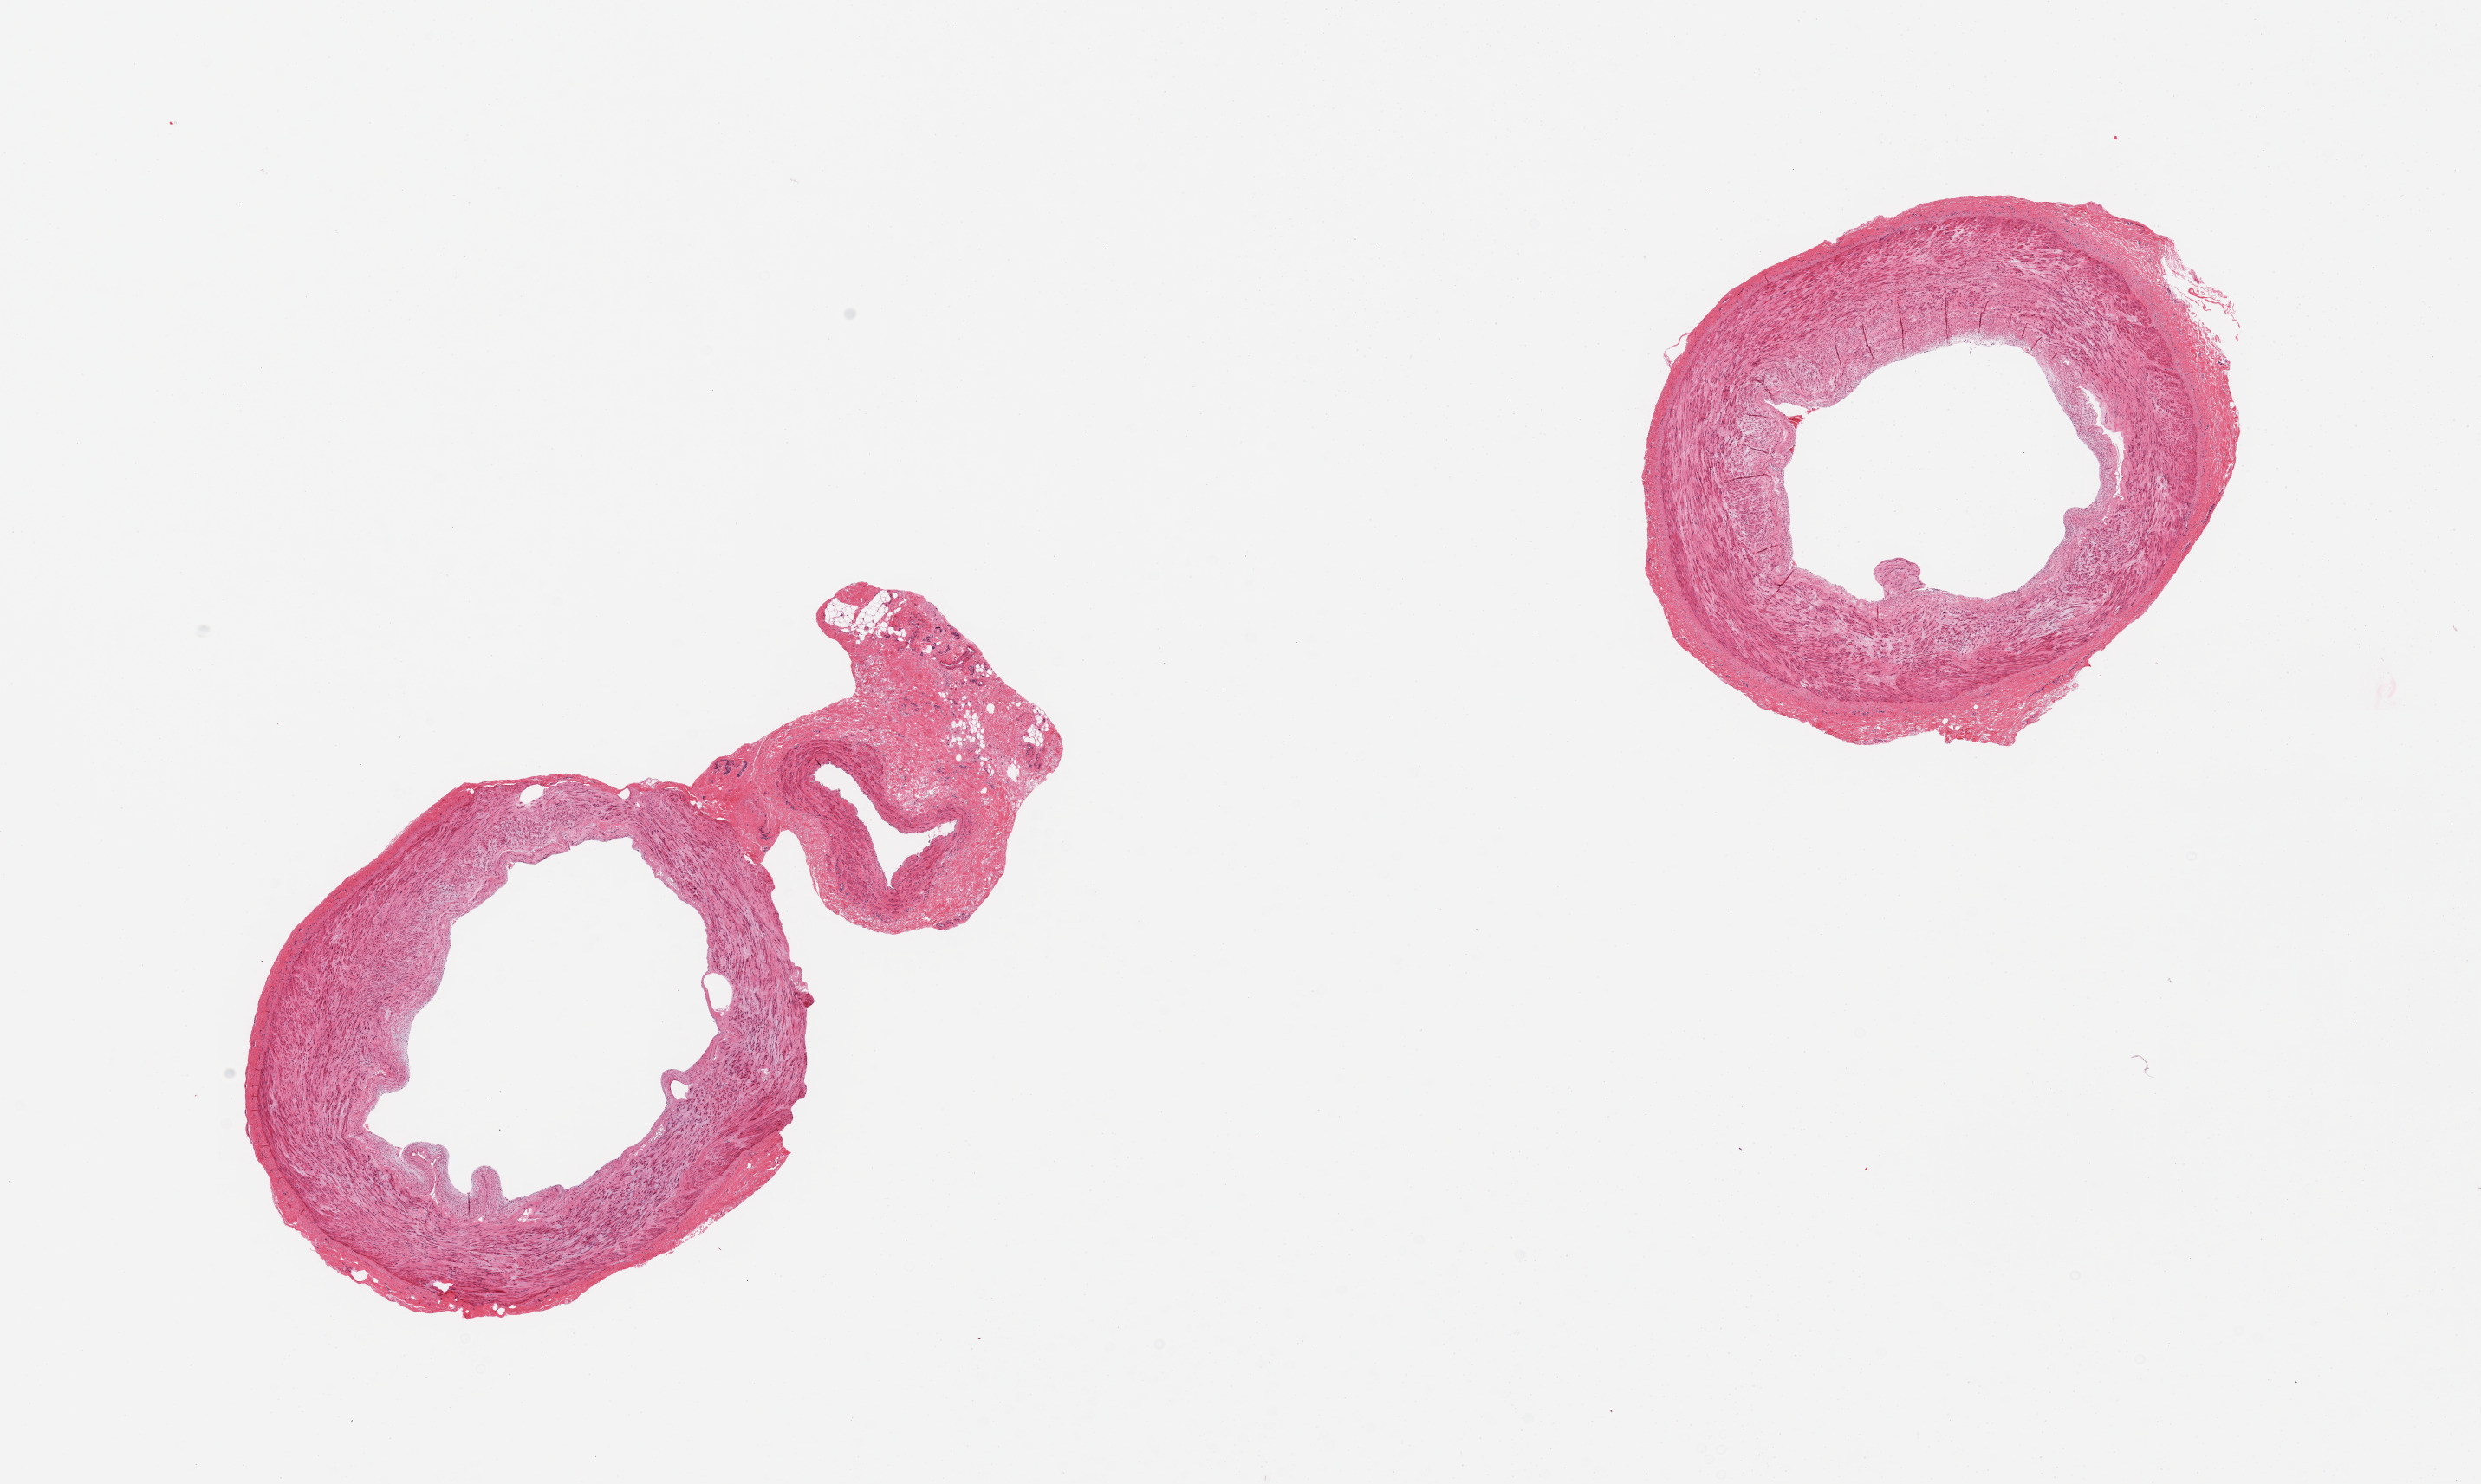
Digitized haematoxylin and eosin-stained section, shown as a low-resolution overview of the whole scanned area (about 22.6 x 13.5 mm), PAXgene-fixed paraffin-embedded (PFPE) section, section of tibial artery (target tissue), donor tissue sample.
• review note (as recorded): 2 pieces; no sclerosis, well trimmed